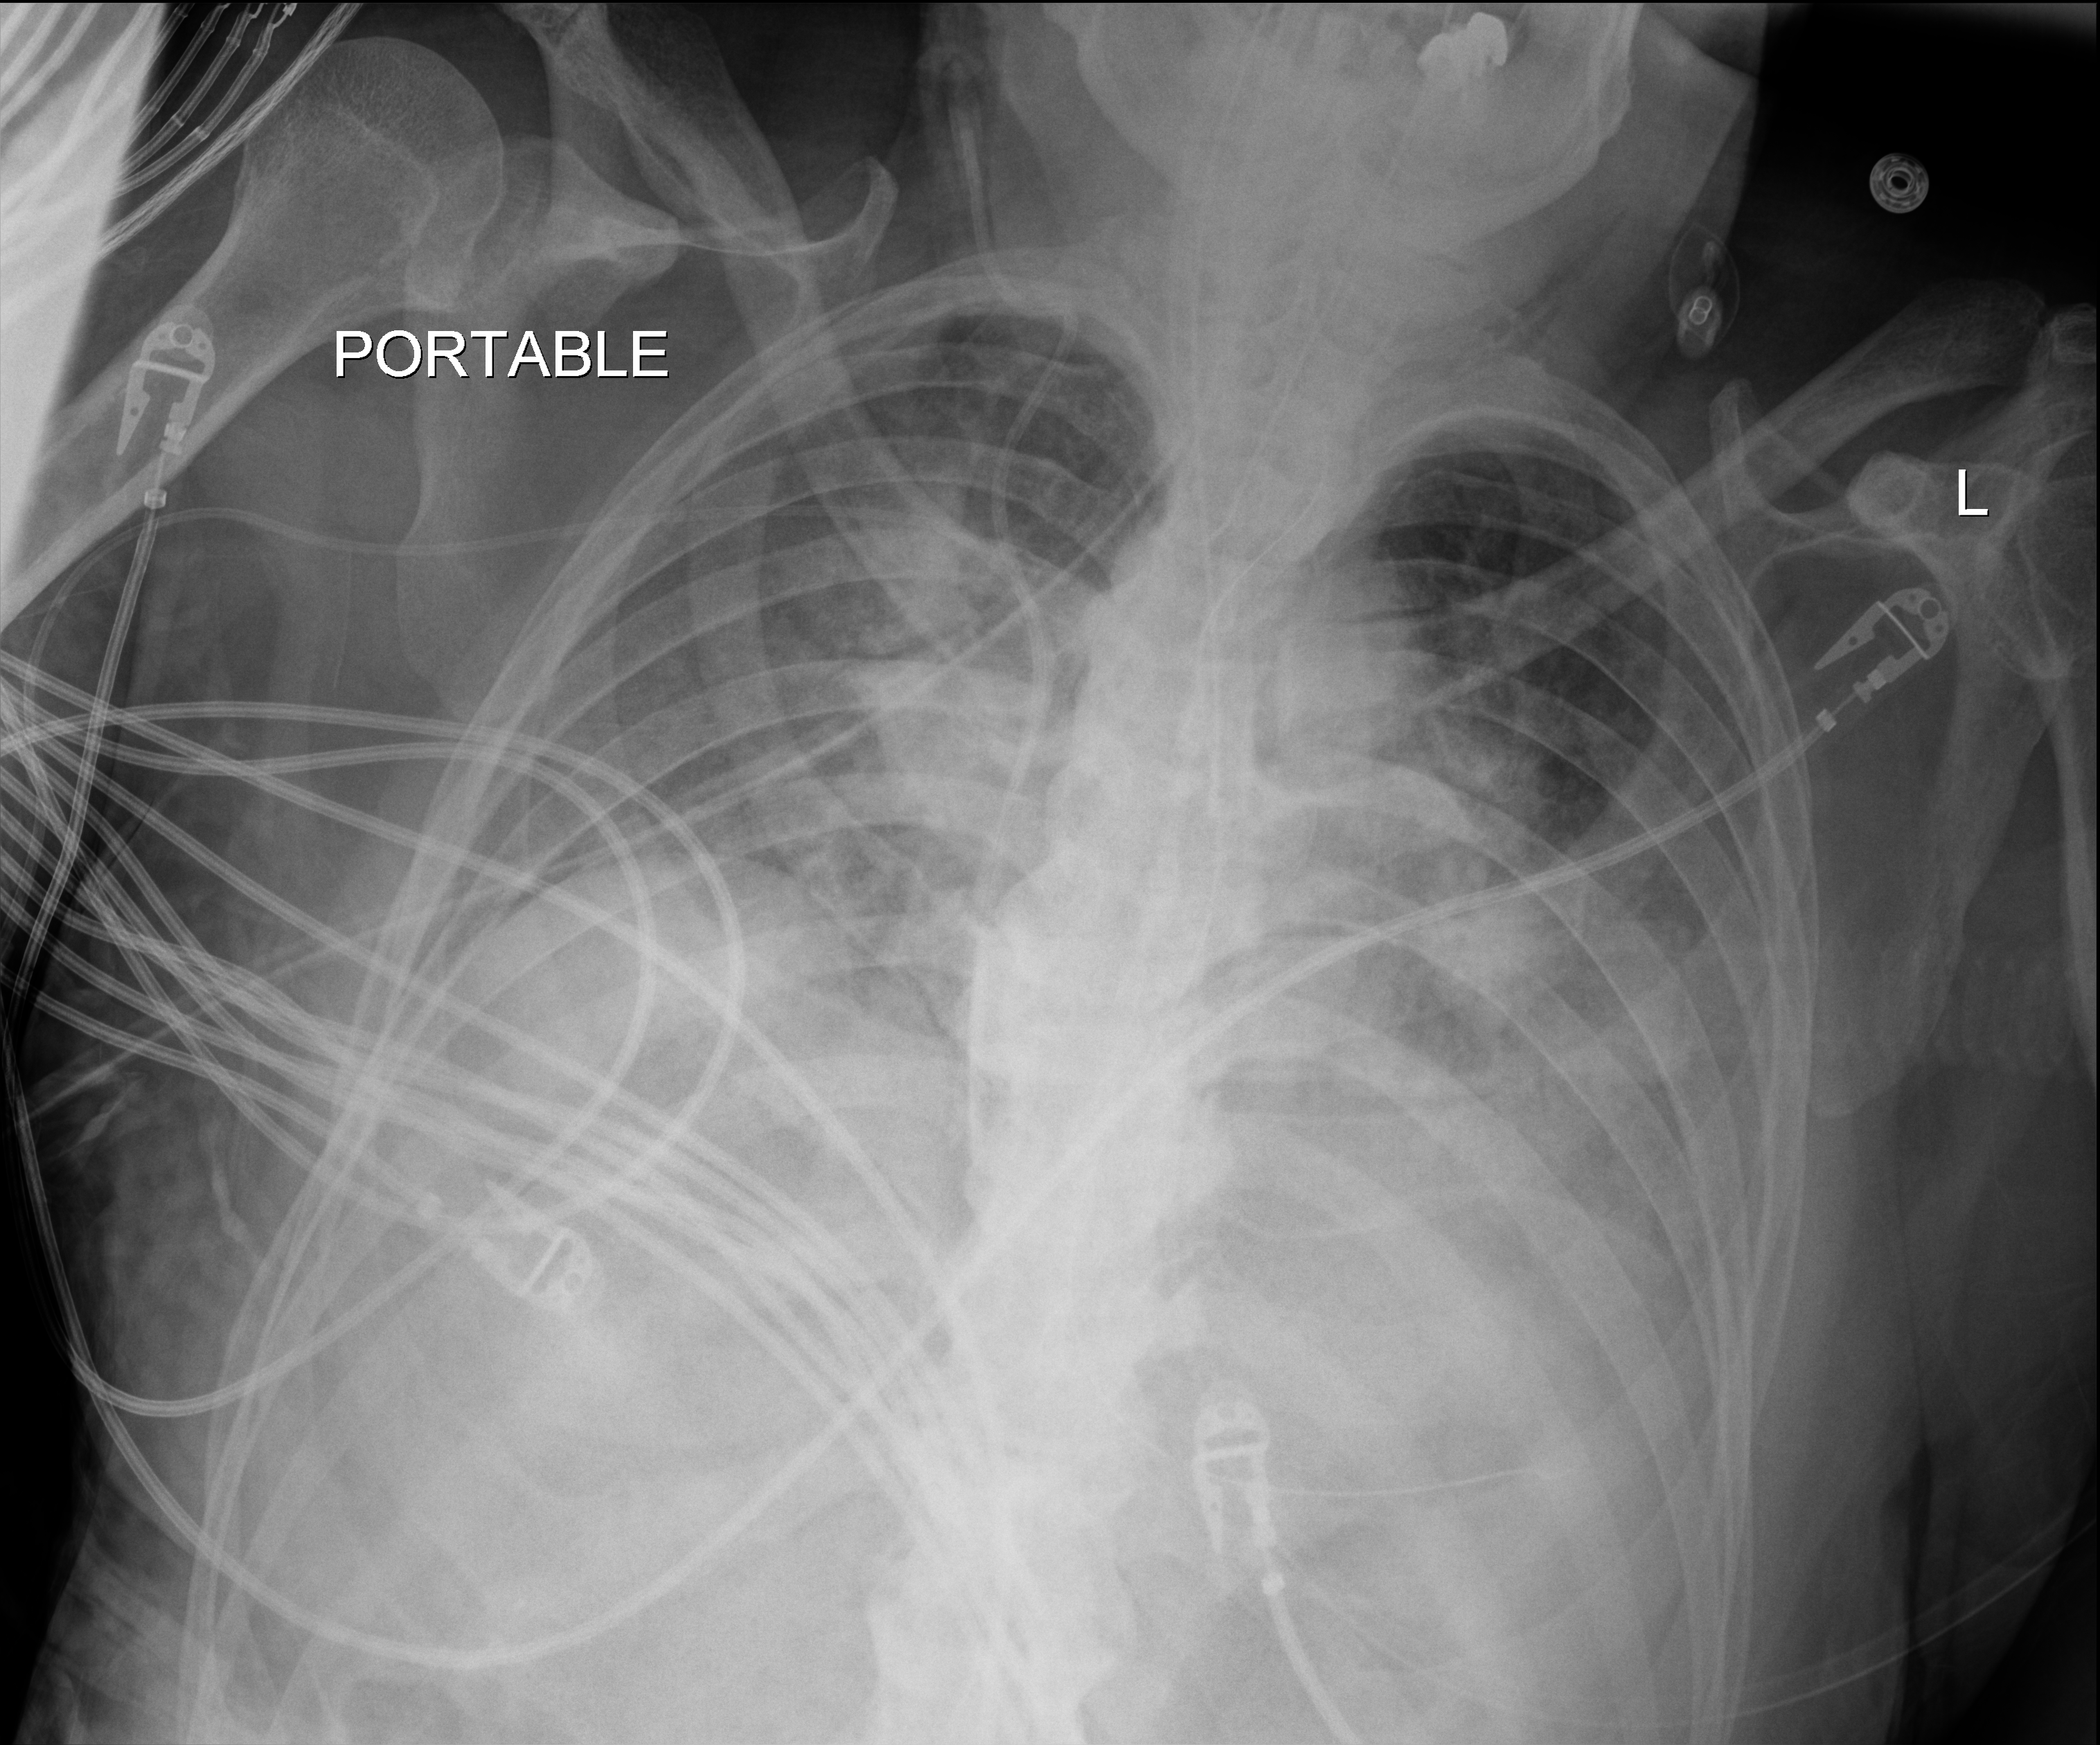
Bedside chest radiograph (digital radiography); anteroposterior (AP) projection. Patient hospitalised with COVID-19; male, aged 75–90 years.
Admission-level facts for this patient (not findings on this image; timing relative to this image not recorded): mechanically ventilated during this hospital stay: yes; admitted to intensive care during this hospital stay: yes.